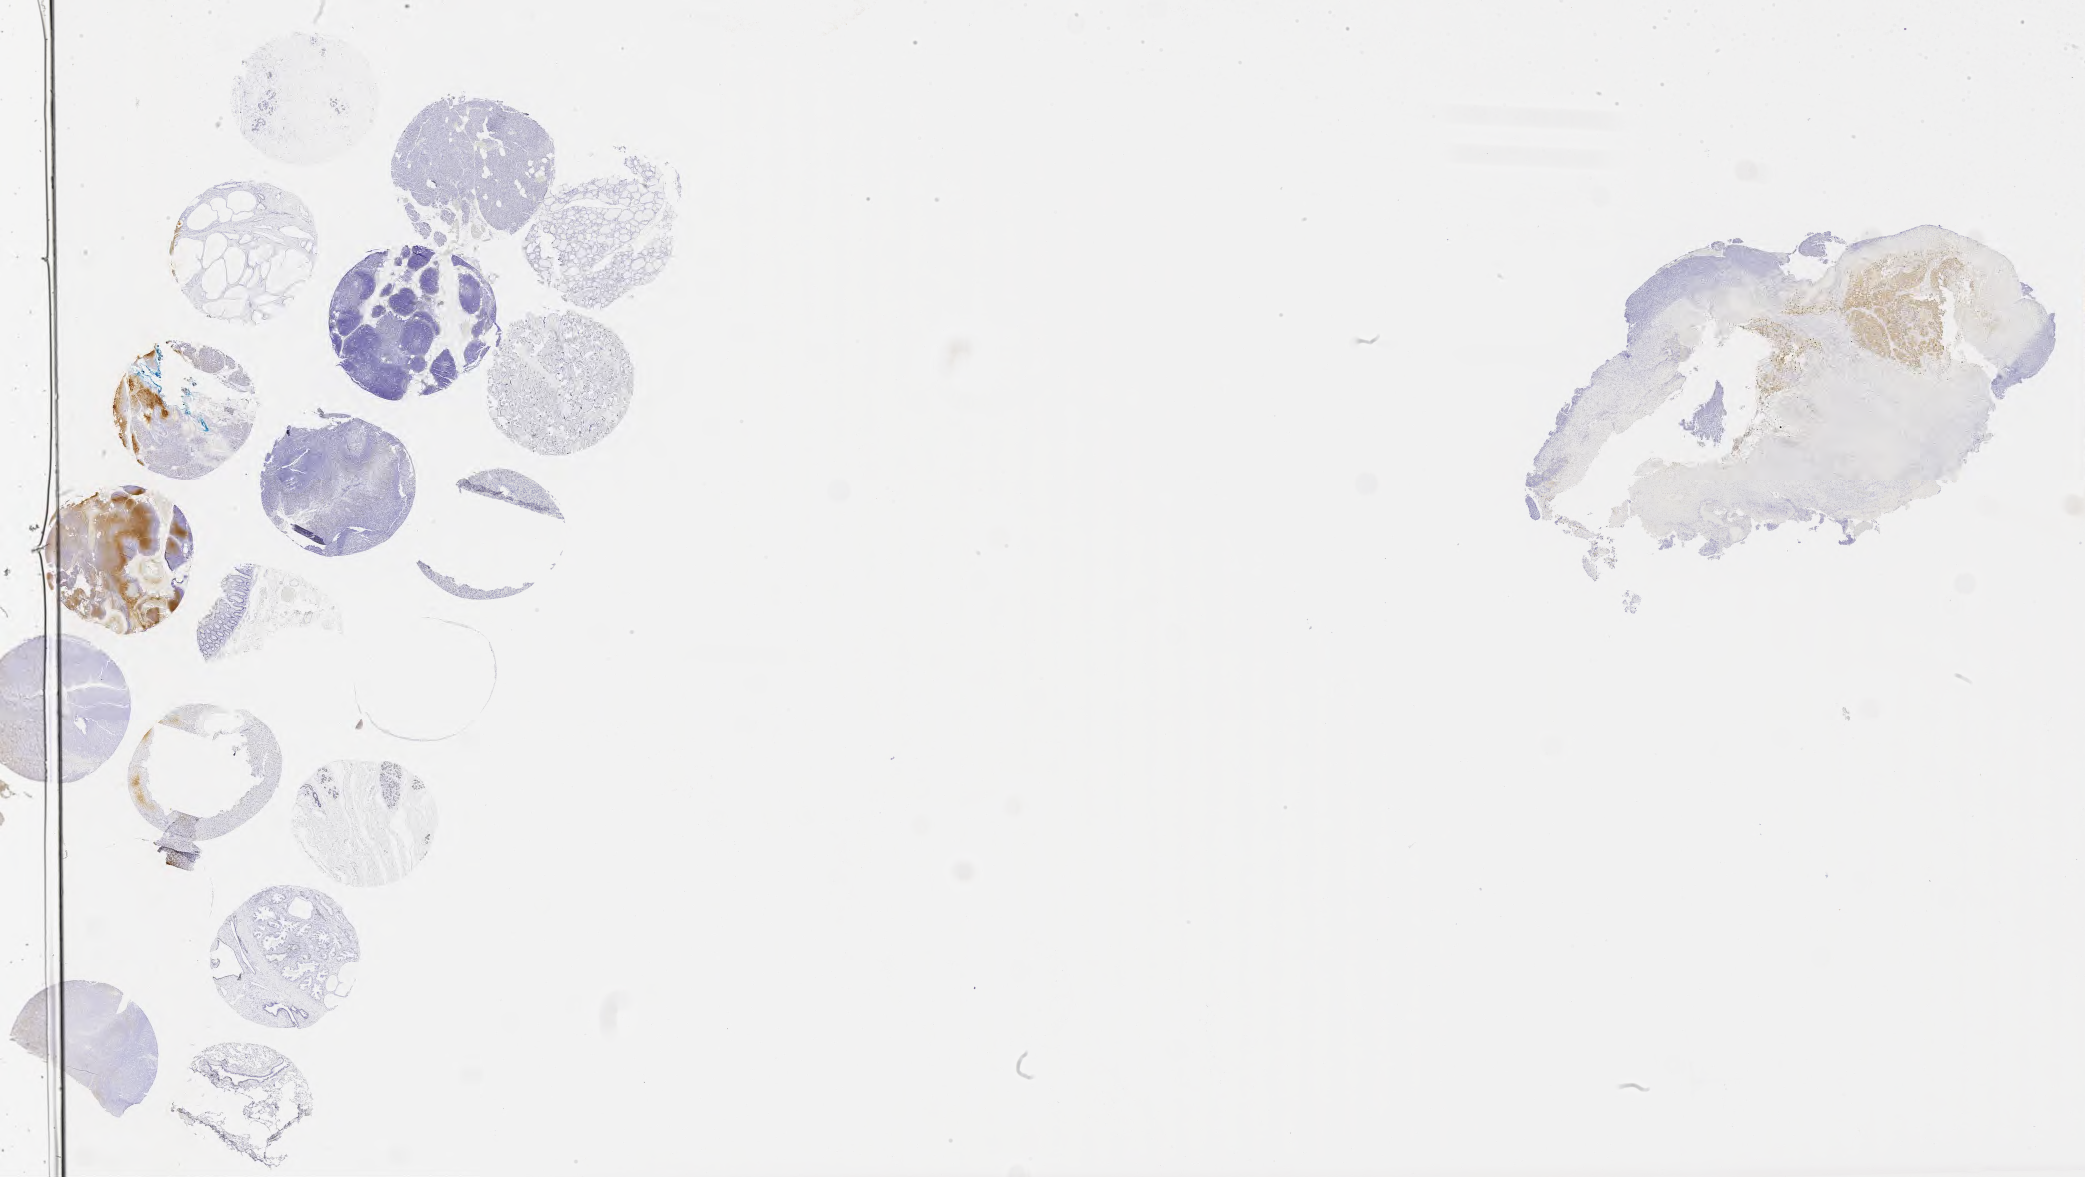
IHC for p63, whole-slide image — low-resolution overview of the scanned area, about 33.7 x 19.0 mm, tumor tissue, site: cervix. Patient: female, age 62 years.
Histologic diagnosis: Squamous cell carcinoma, large cell, nonkeratinizing, NOS.